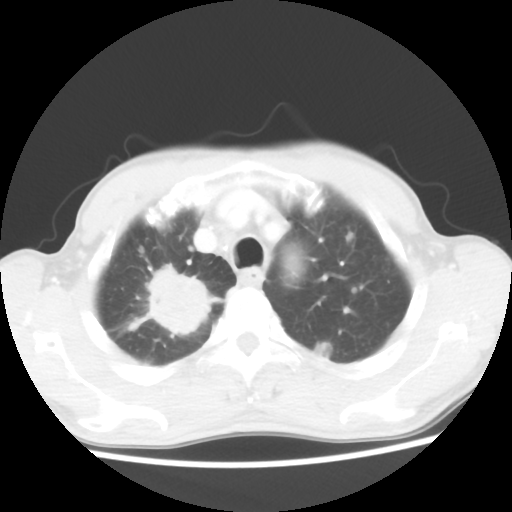
Chest CT, one axial slice. Position 43 of 52 along the scan axis. Reconstruction kernel STANDARD. 100 kVp. Lung window (W 1500 / L -600 HU). 5 mm slice thickness. 512 × 512 image matrix, field of view 323 × 323 mm. Patient: male, 66 years. From the clinical record (not read from this slice): clinical TNM (as recorded): T2 N0 M1a.
Structures marked on this image (bounding box drawn by a radiologist):
- lung tumour (recorded histology: adenocarcinoma): bounding box <126,261,216,334> (left, top, right, bottom; pixels)